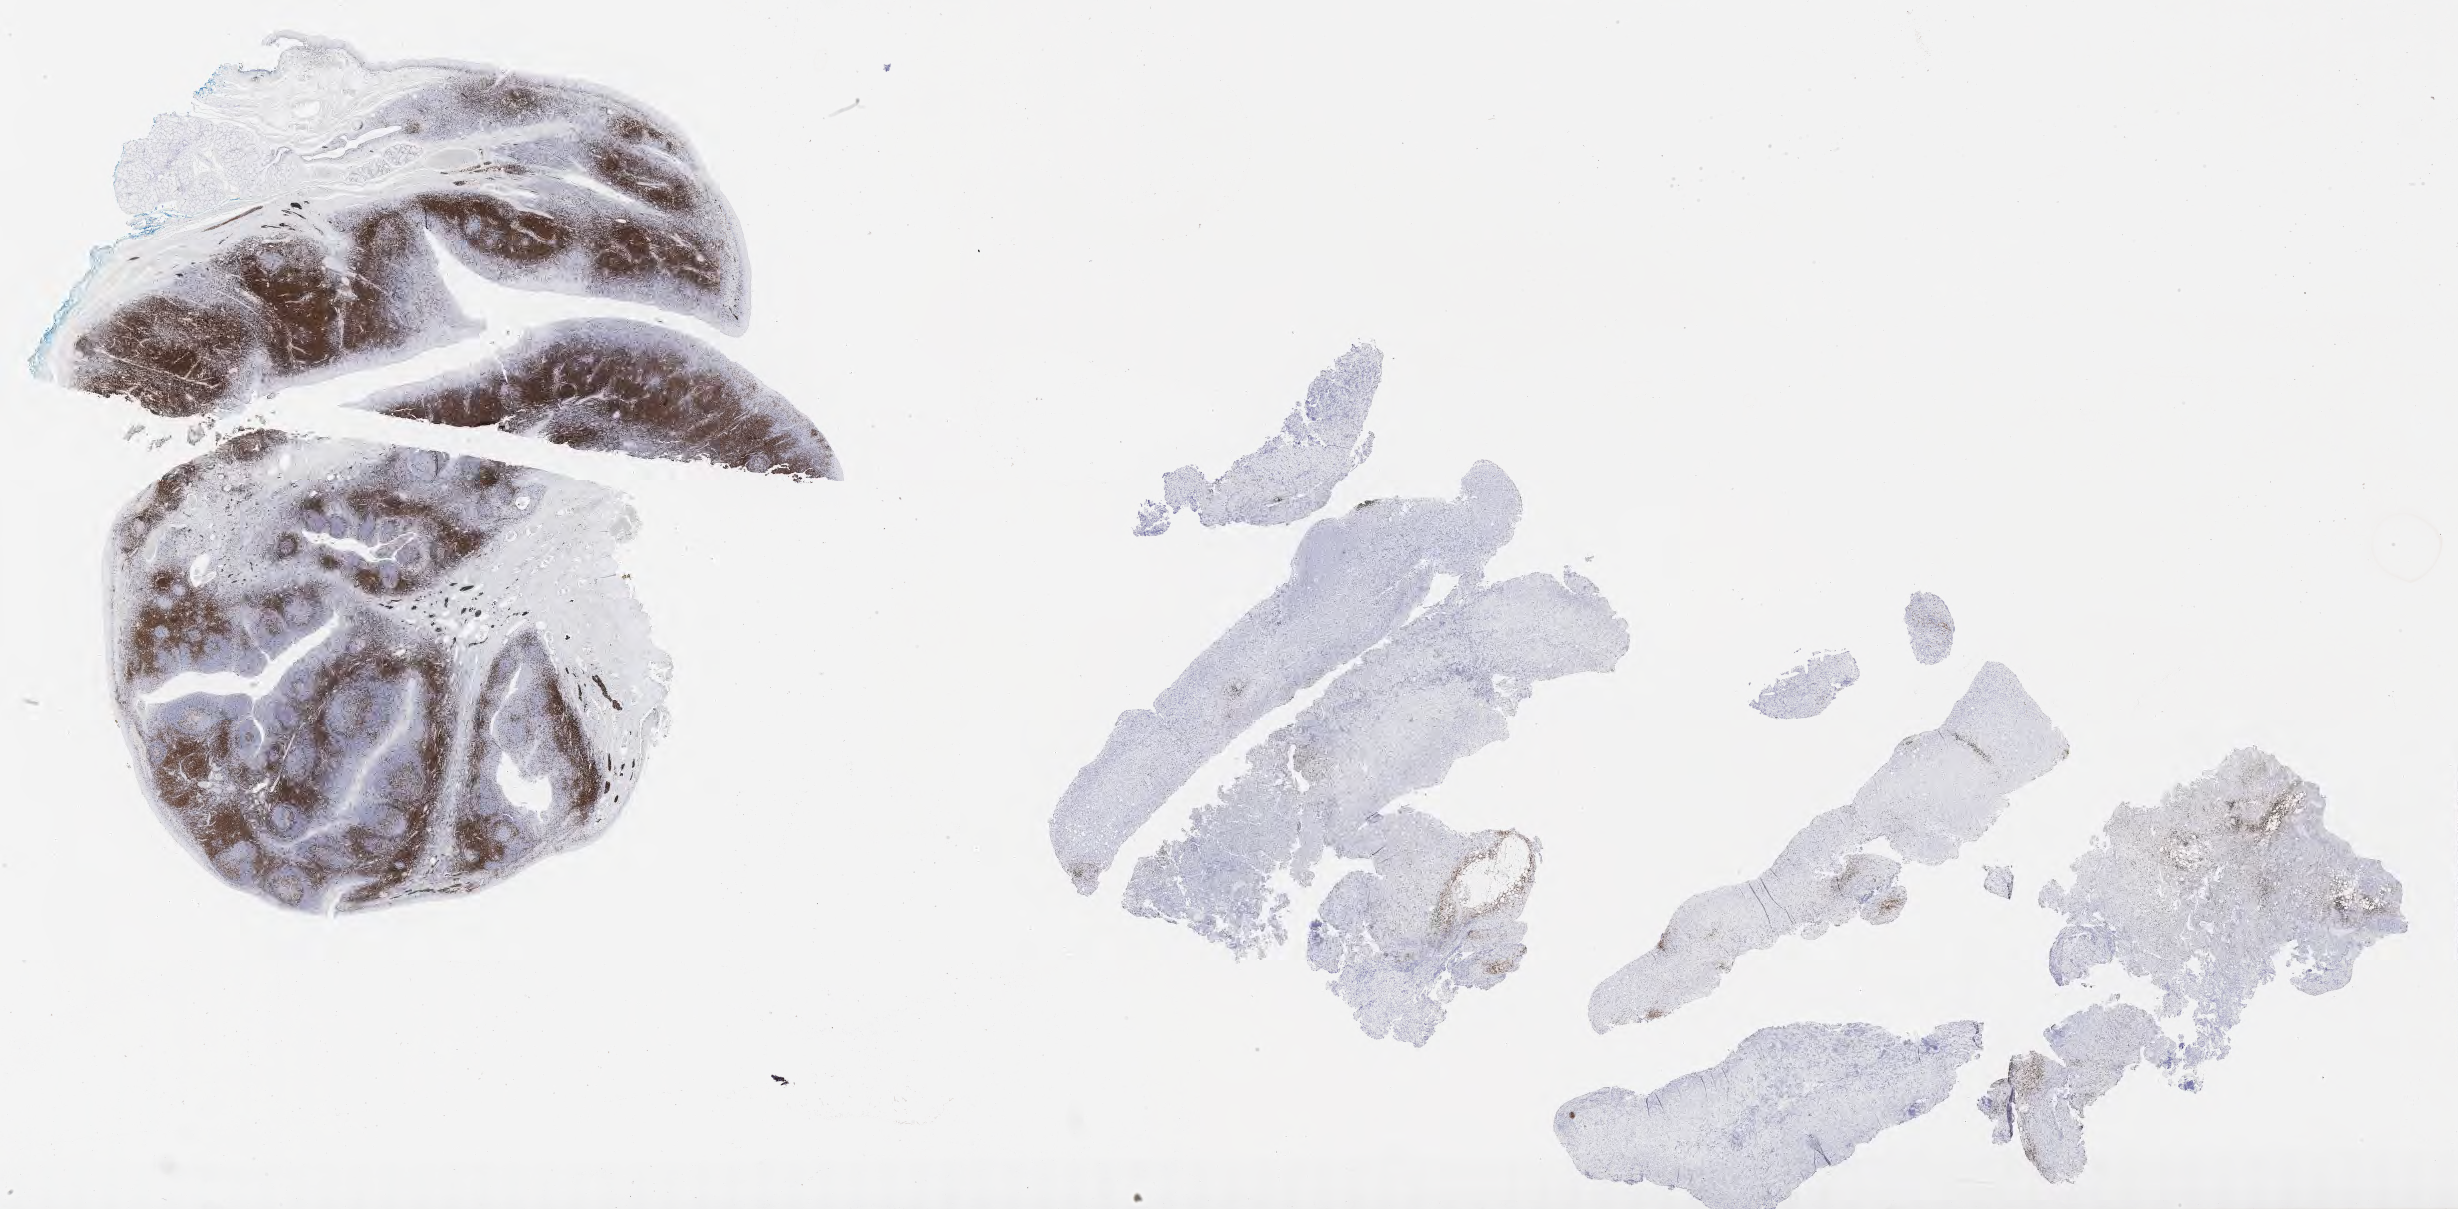
Immunohistochemistry (IHC) whole-slide image stained for CD3 — low-resolution overview of the scanned area, about 39.8 x 19.6 mm; specimen: tumor tissue. Male patient, age 45 years.
Histologic diagnosis: Diffuse large B-cell lymphoma, NOS.